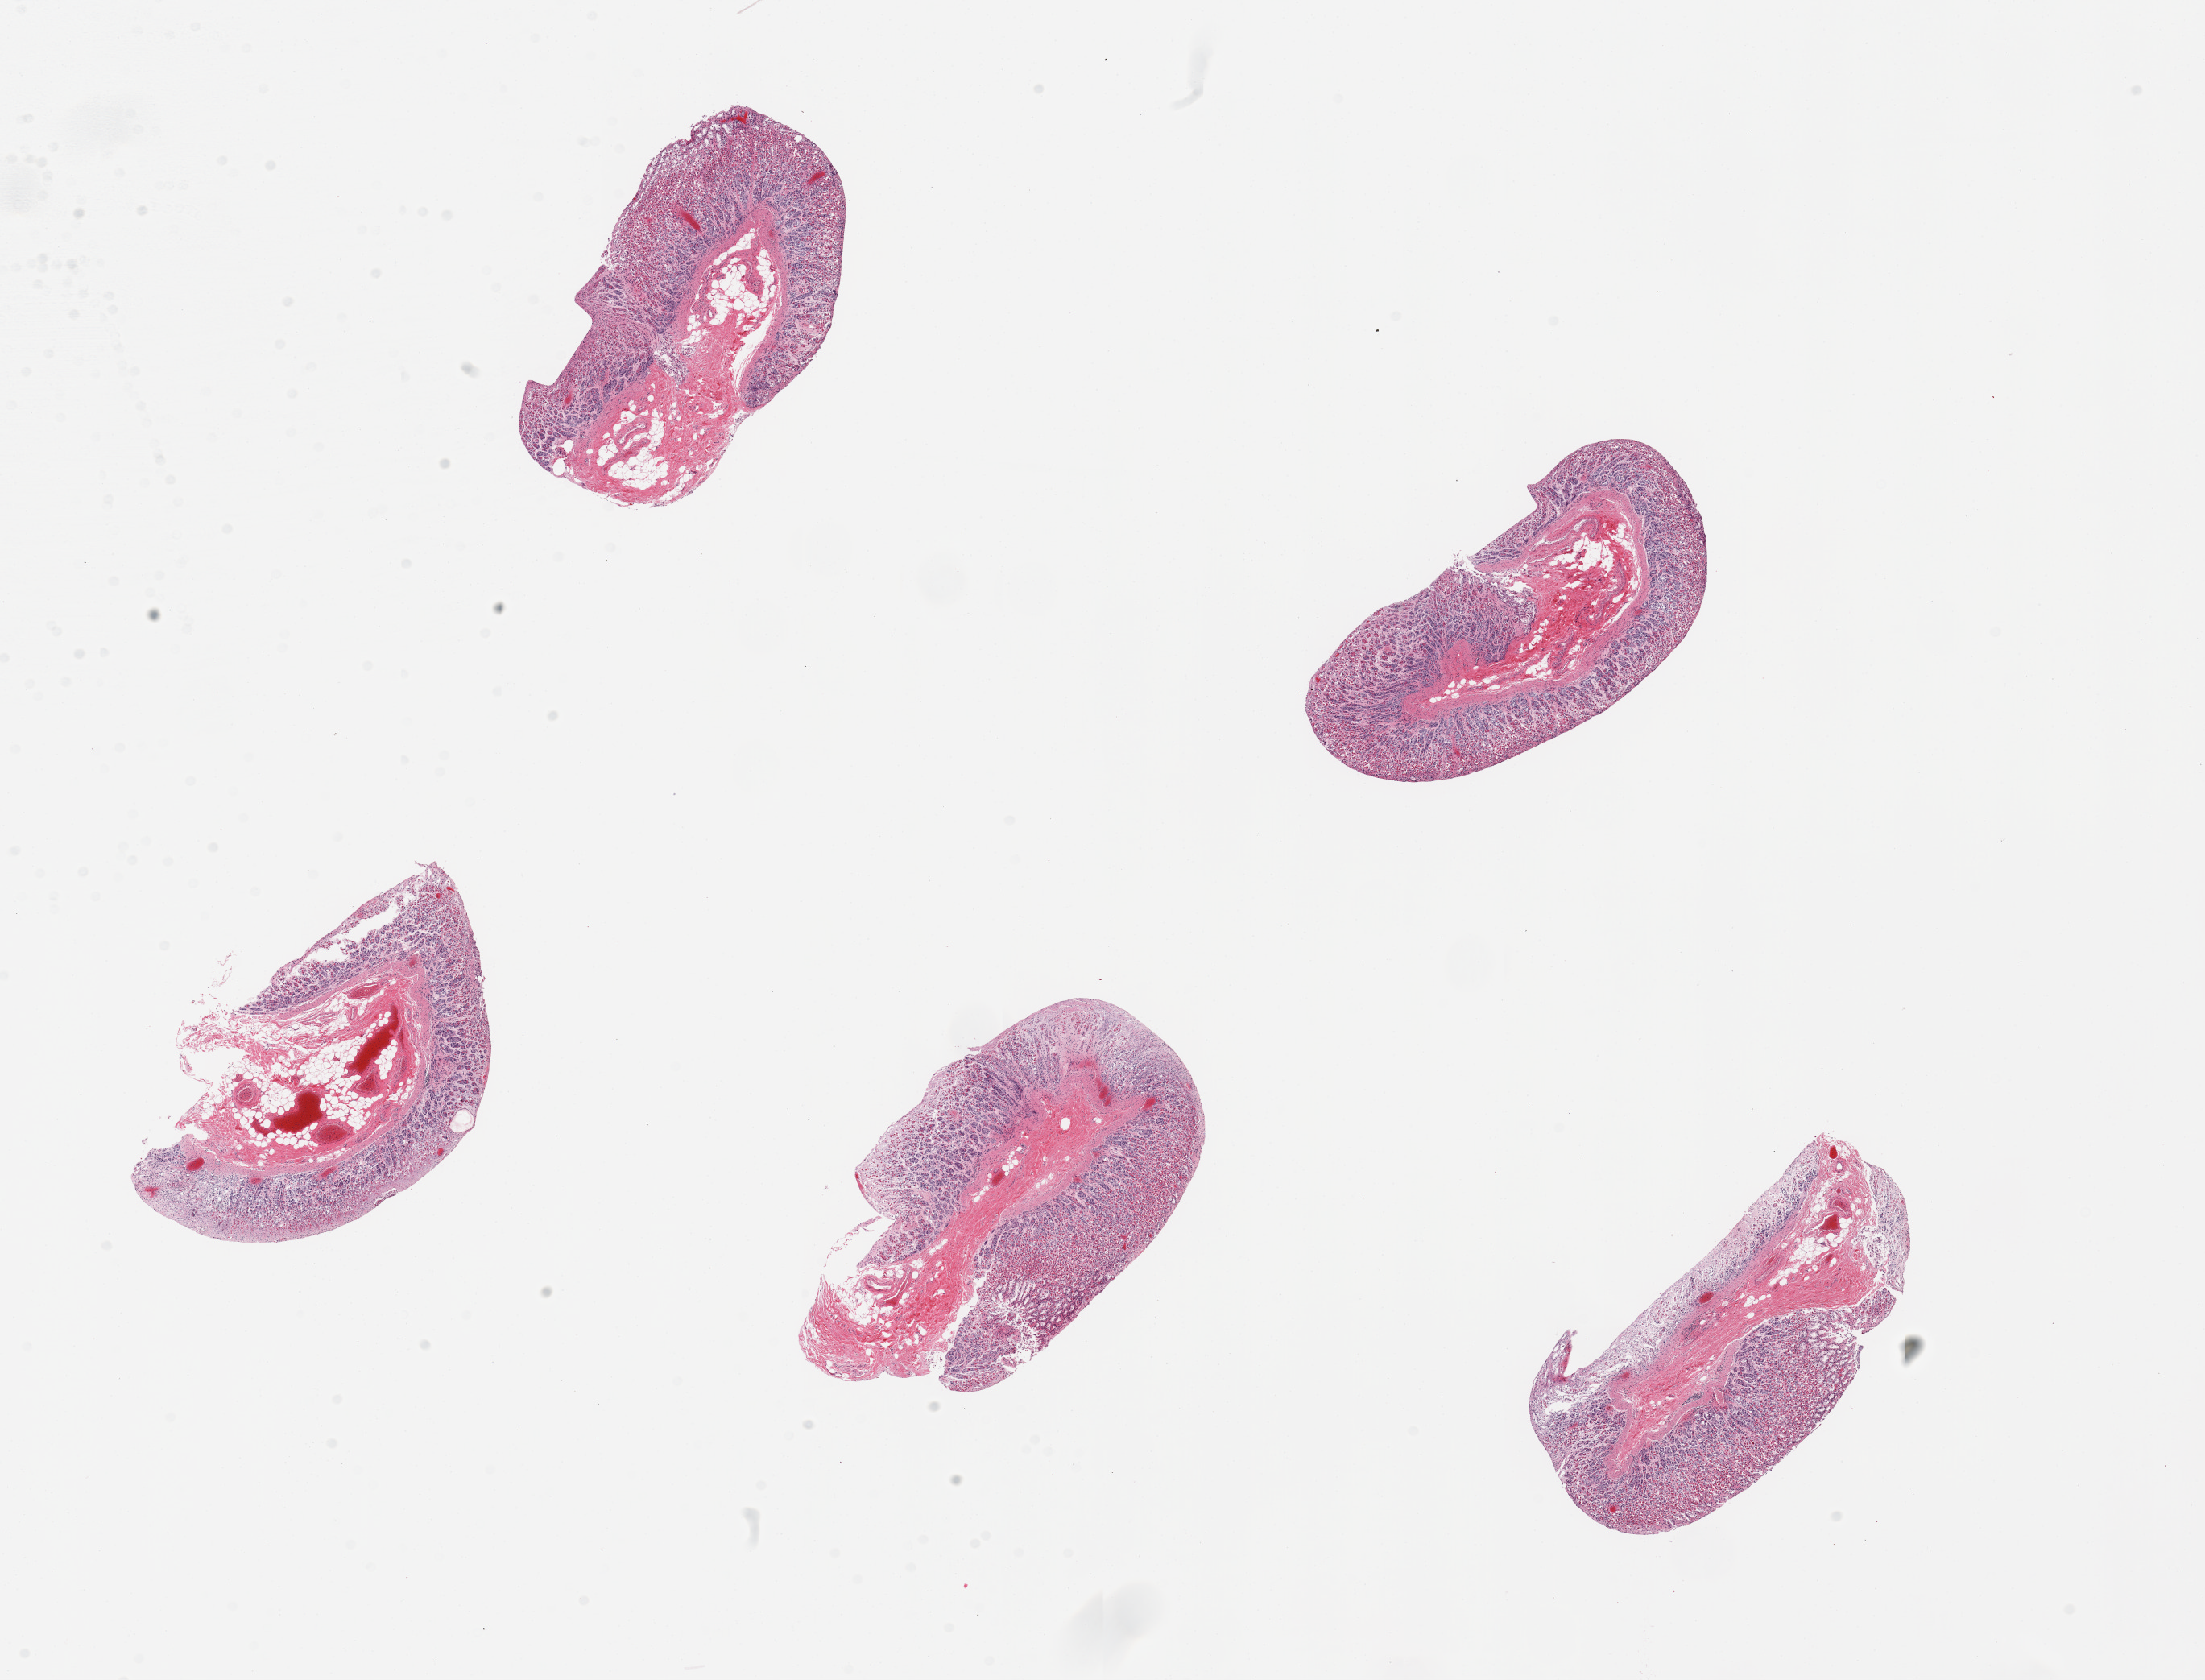
Digitized haematoxylin and eosin-stained section, brightfield — a low-resolution overview of the entire scanned area, about 21.7 x 16.5 mm (slide scanned at 20x). PAXgene-fixed paraffin-embedded (PFPE) section. Section of stomach (target tissue). Tissue donor sample. Donor sex: male.
Pathologist's review note for this sample: 5 pieces; mucosa and submucosa, moderate to focally severe autolysis.